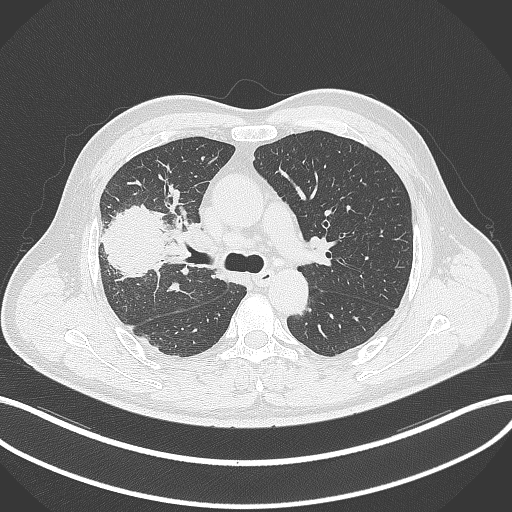
Chest CT, one axial slice. Position 216 of 348 along the scan axis. Lung window (W 1500 / L -600 HU). 1 mm slice thickness. 512 × 512 image matrix, field of view 400 × 400 mm. Patient: male, 55 years. From the clinical record (not read from this slice): clinical TNM (as recorded): T3 N2 M1.
Structures marked on this image (bounding box drawn by a radiologist):
- lung tumour (recorded histology: adenocarcinoma): box from (x=95, y=202) to (x=168, y=282) px